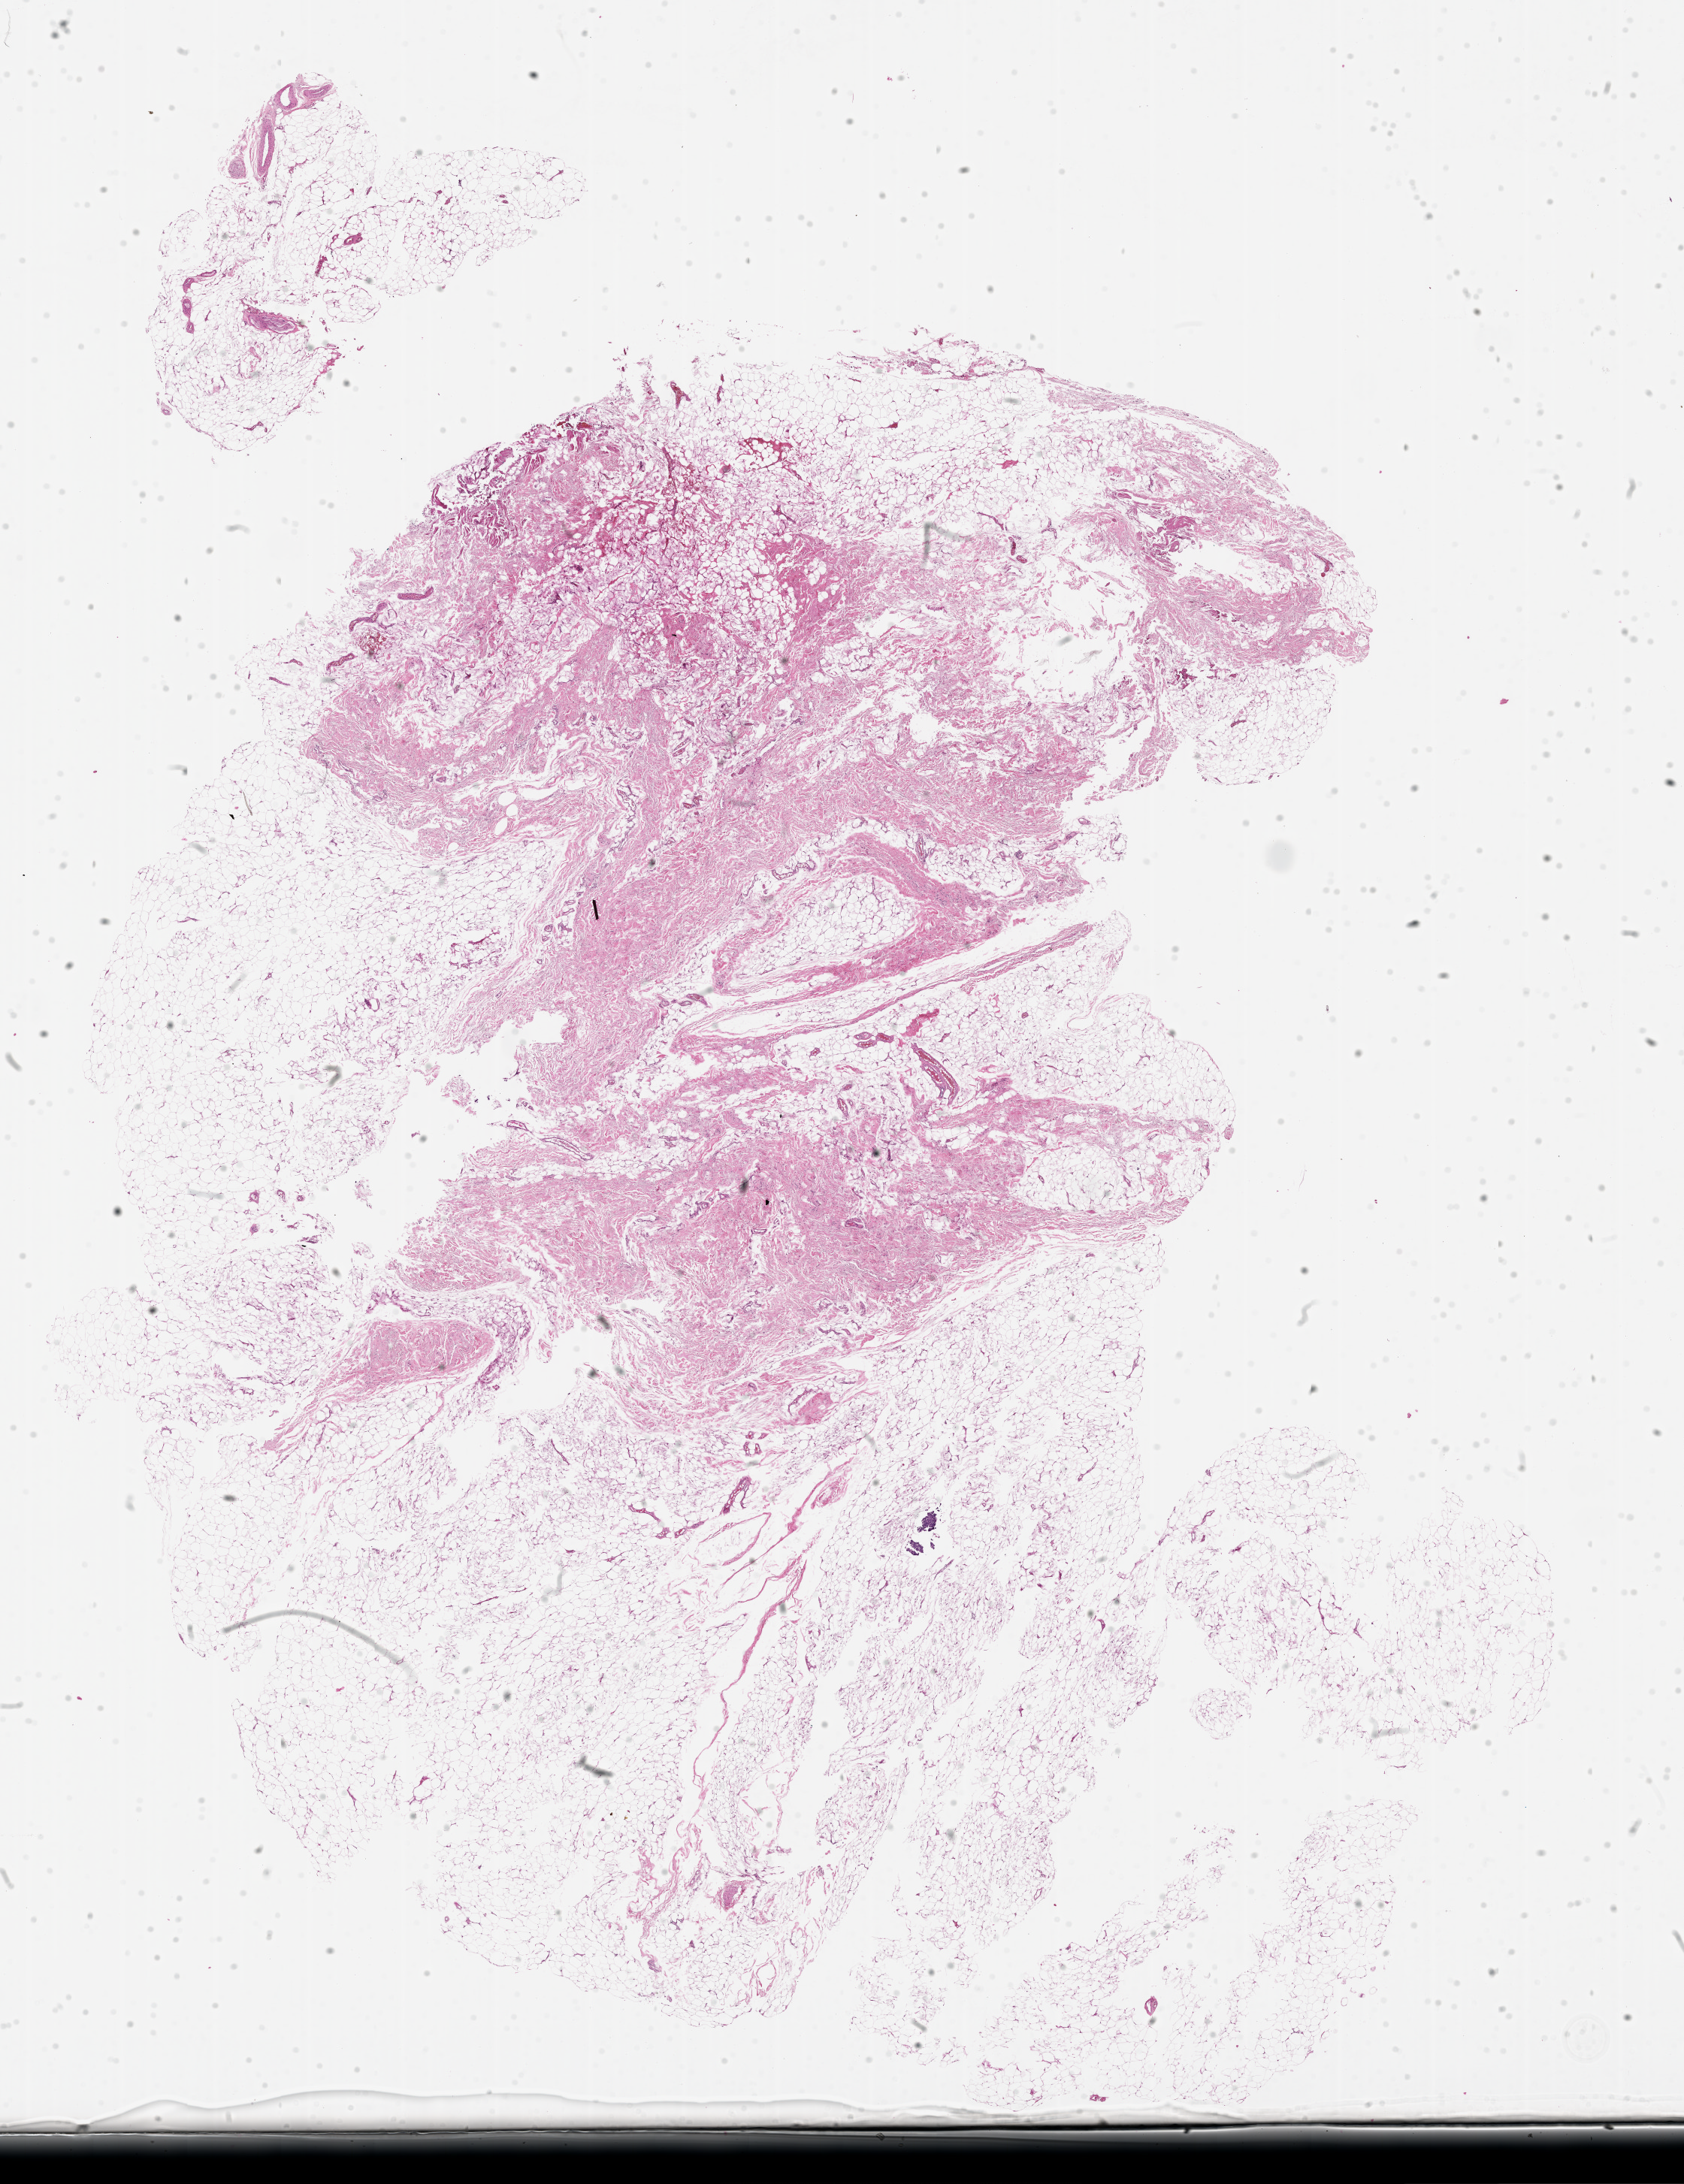
H&E whole-slide image — whole scanned area (about 18.0 x 23.4 mm, slide scanned at 20x) shown as a low-resolution overview; normal (non-tumour) tissue sample, sampled site: lymph node. Patient: male, age 41 years.
This section: normal (non-tumour) tissue from the same patient. Patient diagnosis: Malignant melanoma, NOS.